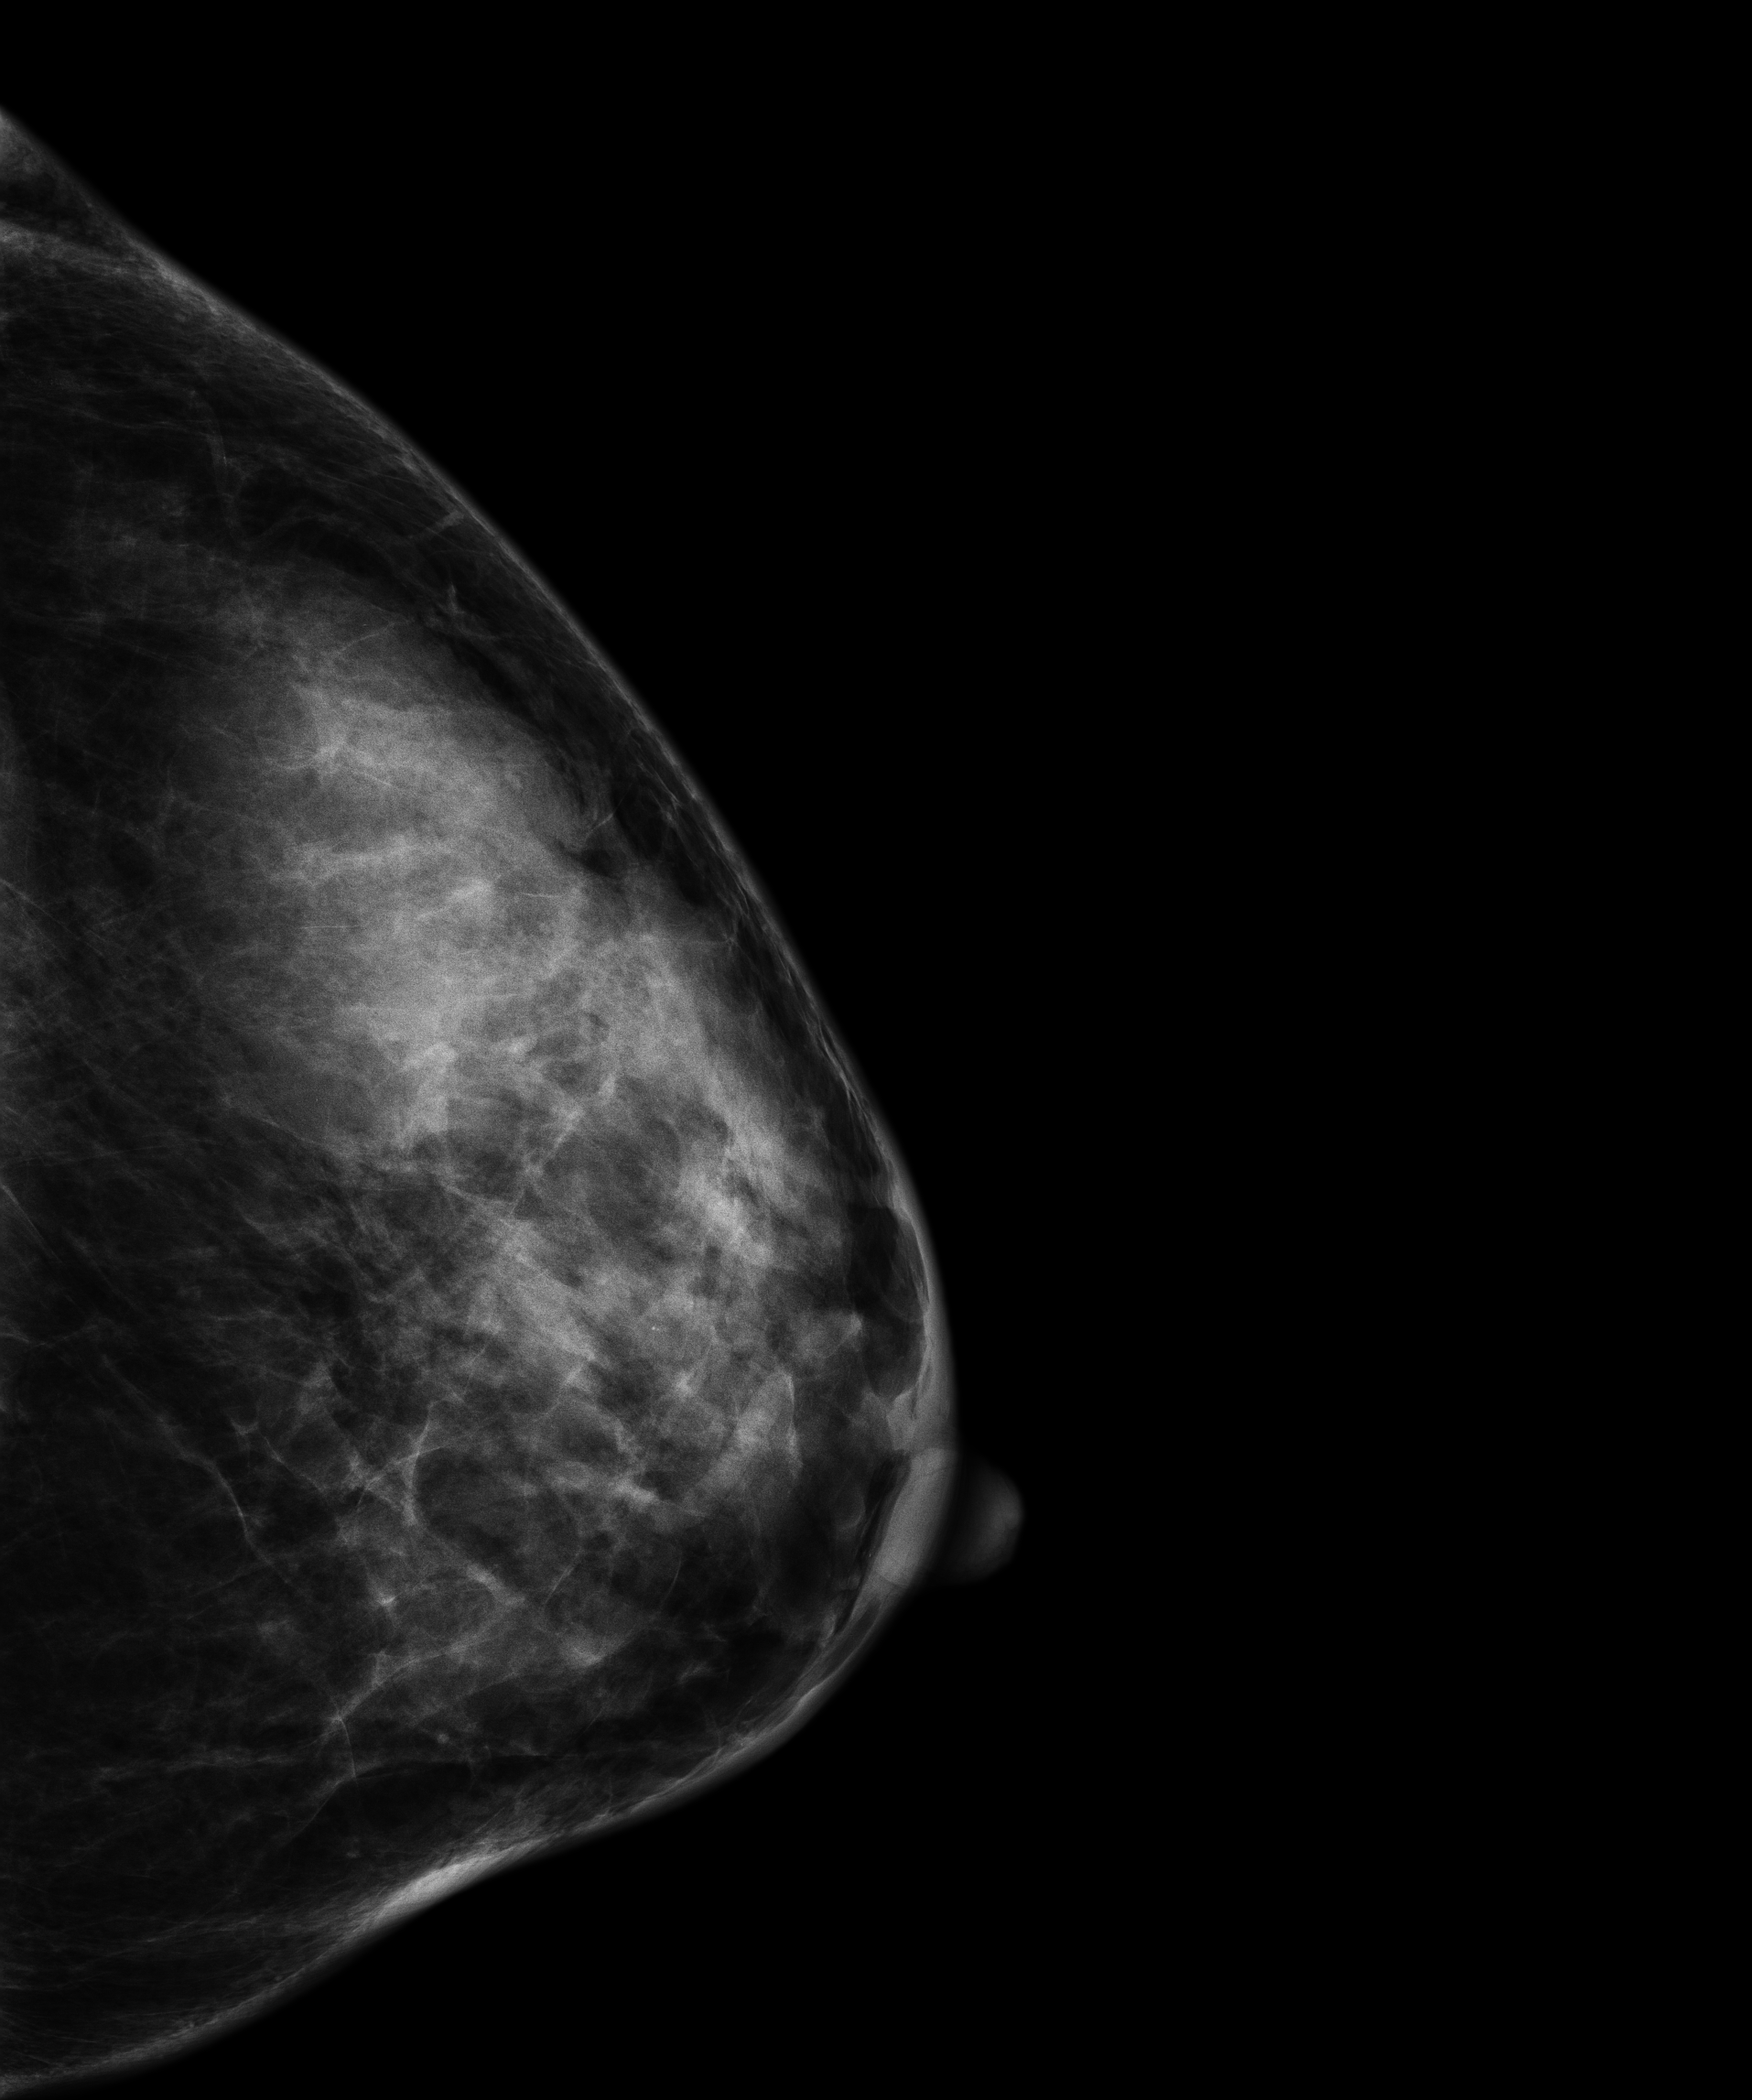
Digital mammogram (FFDM), left breast, craniocaudal (CC) view, screening examination, compressed breast thickness 43 mm. Patient aged 55 years (female).
- breast density at the screening exam (both breasts): heterogeneously dense (BI-RADS density category c)
- final BI-RADS assessment for this screening round (tomosynthesis exam, both breasts): category 1
- recall: no recall after this screen